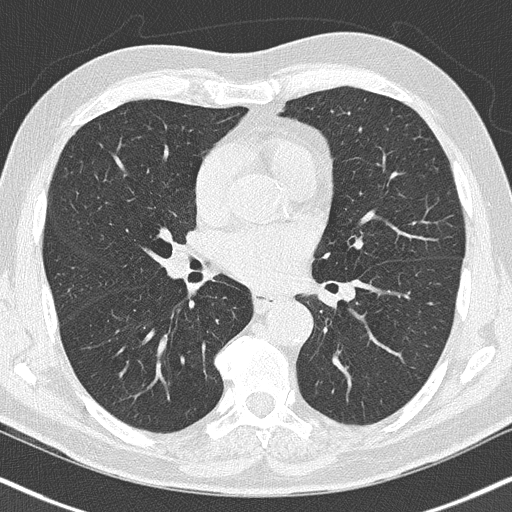
Low-dose screening chest CT, axial slice, first (baseline) screen, lung window (W 1500 / L -600 HU), lung (sharp) reconstruction kernel (B50f), 120 kVp, slice 91 of 186 in the series. Male participant, aged 66 years at enrolment. Current smoker at enrolment.
- Expert-annotated lung lesion, bounding box (x1, y1, x2, y2) in pixels: (185, 273, 205, 296).
- Screening reader's record for this exam (one nodule recorded; not confirmed to be the boxed lesion): non-calcified nodule or mass ≥4 mm, right upper lobe, 5 × 4 mm, smooth margins.
- Lung cancer was diagnosed 778 days after this screen: squamous cell carcinoma, NOS, right lower lobe, poorly differentiated (G3), stage IIA (AJCC 6th edition), 22 mm at pathology.